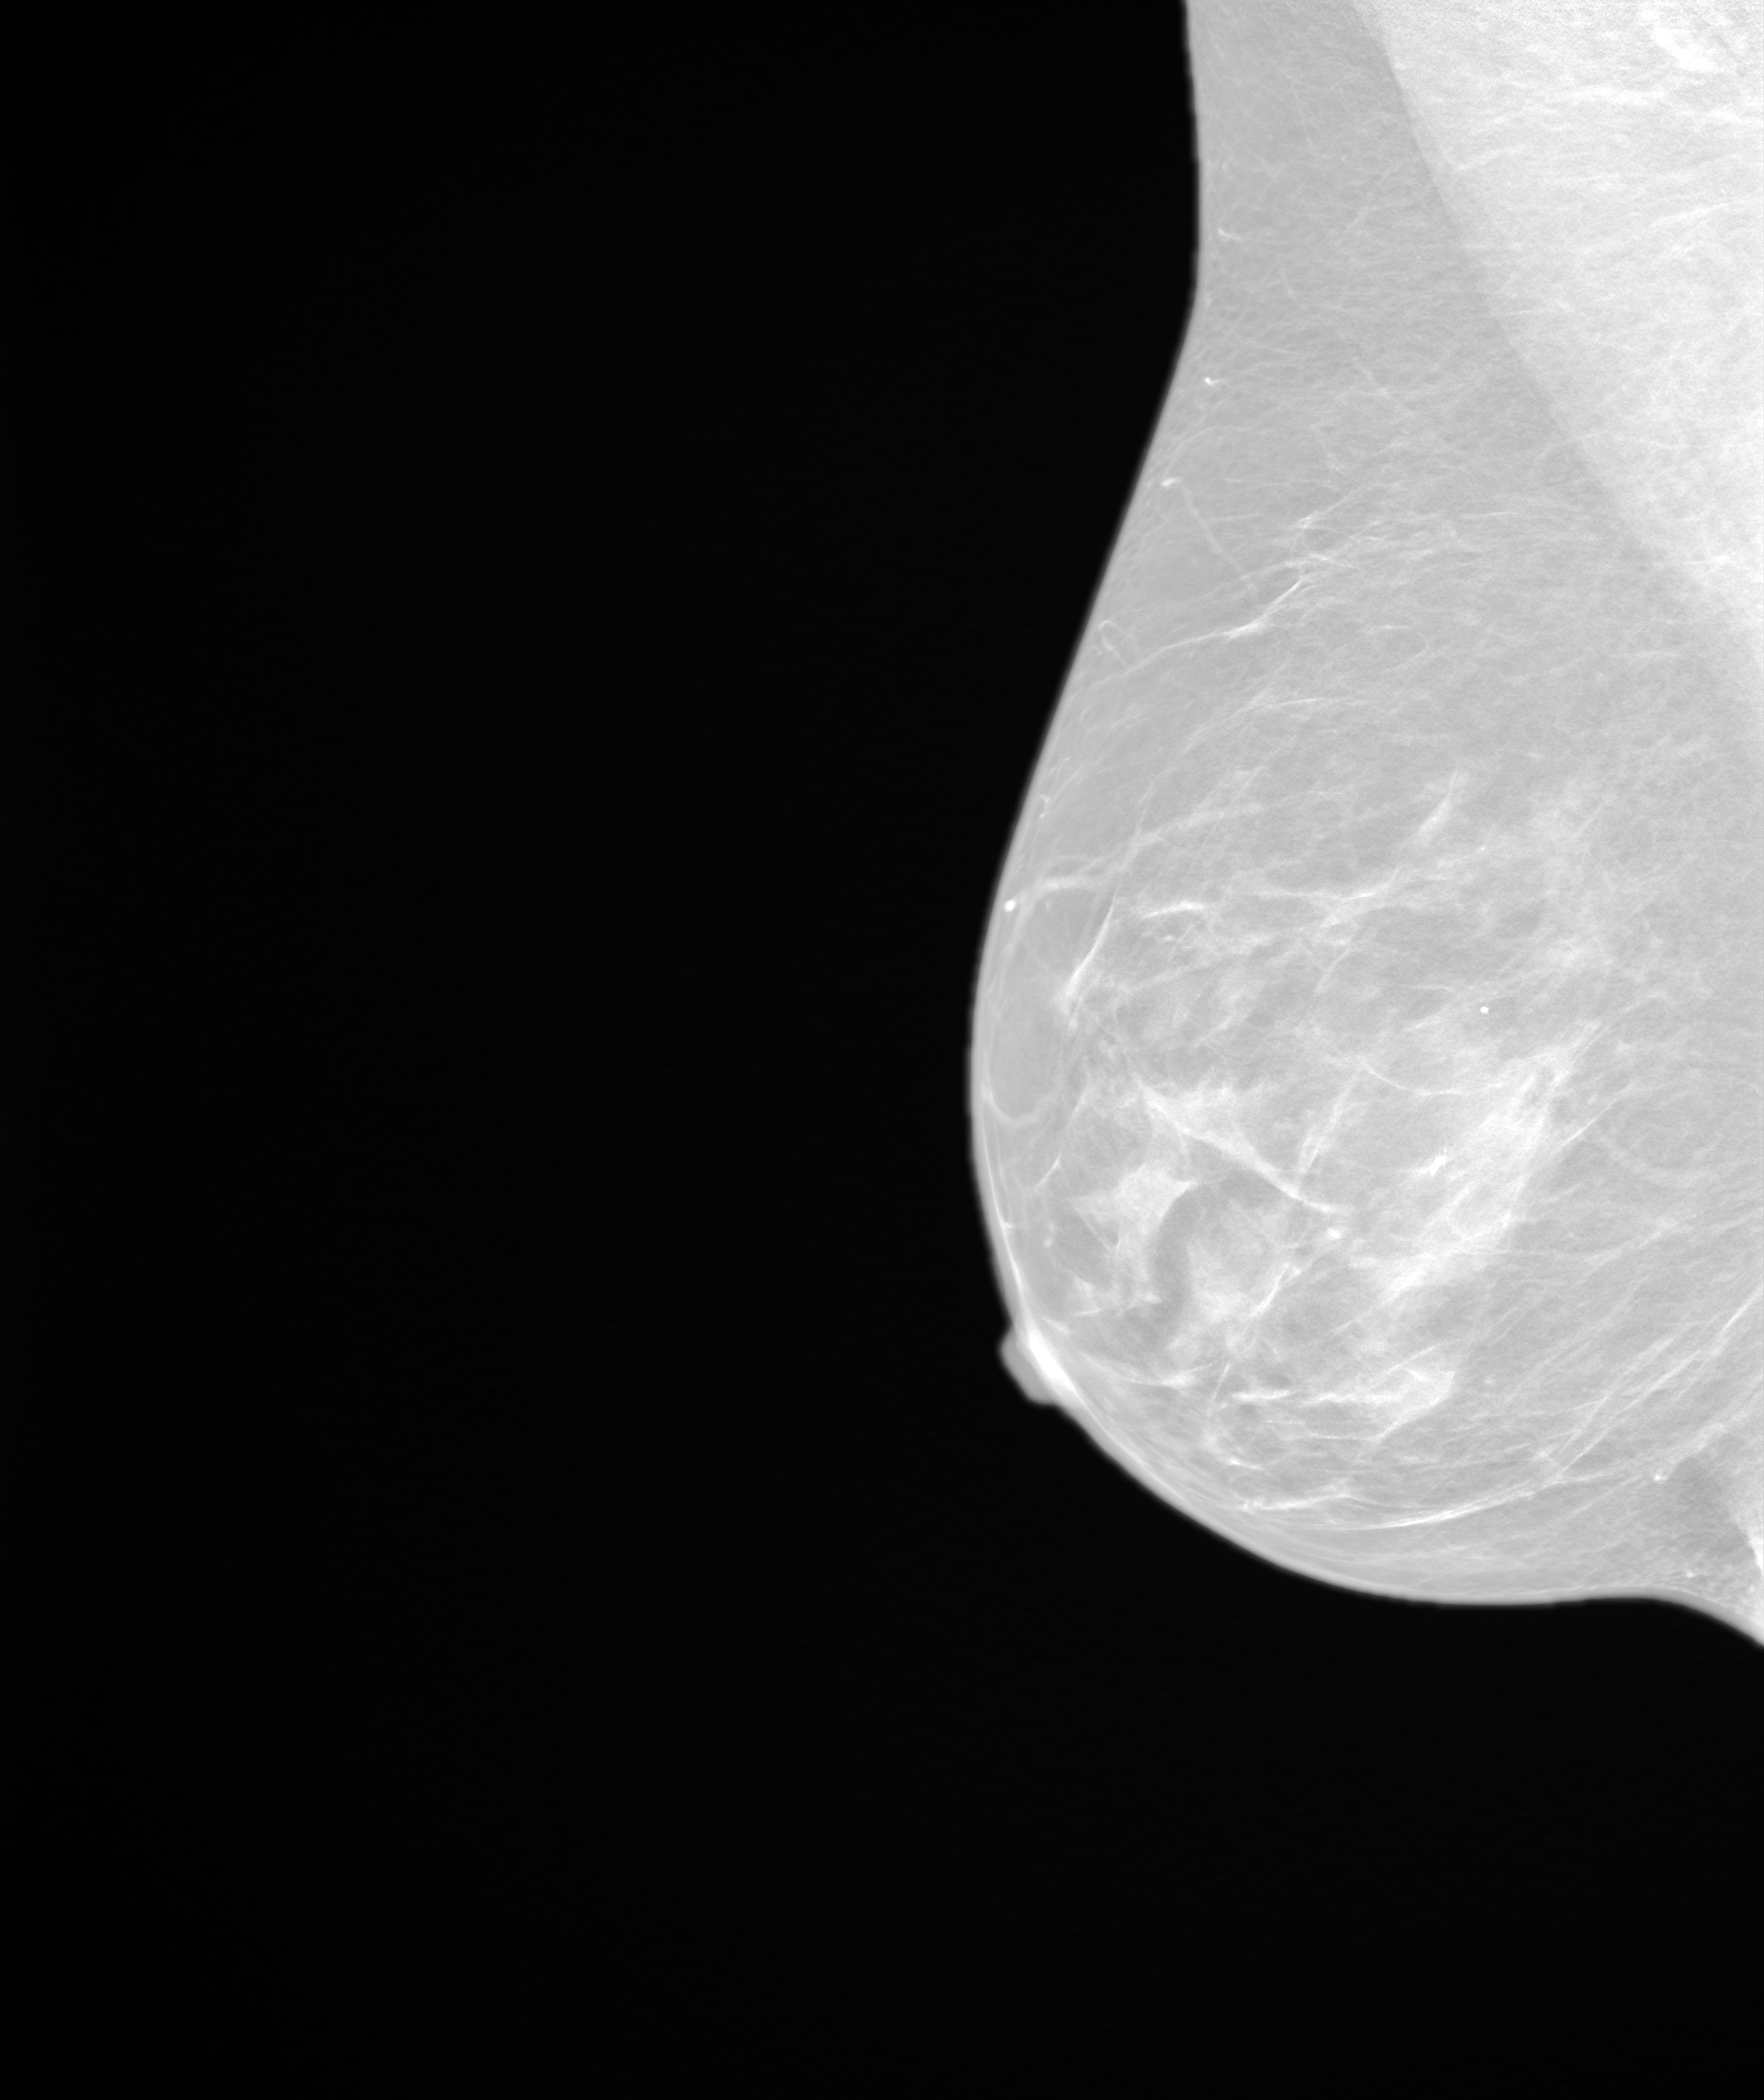
Annual screening mammography examination. Female patient, age 49 years.
Image type: synthesized 2-D view from tomosynthesis. Breast: right. Projection: mediolateral oblique (MLO) view.